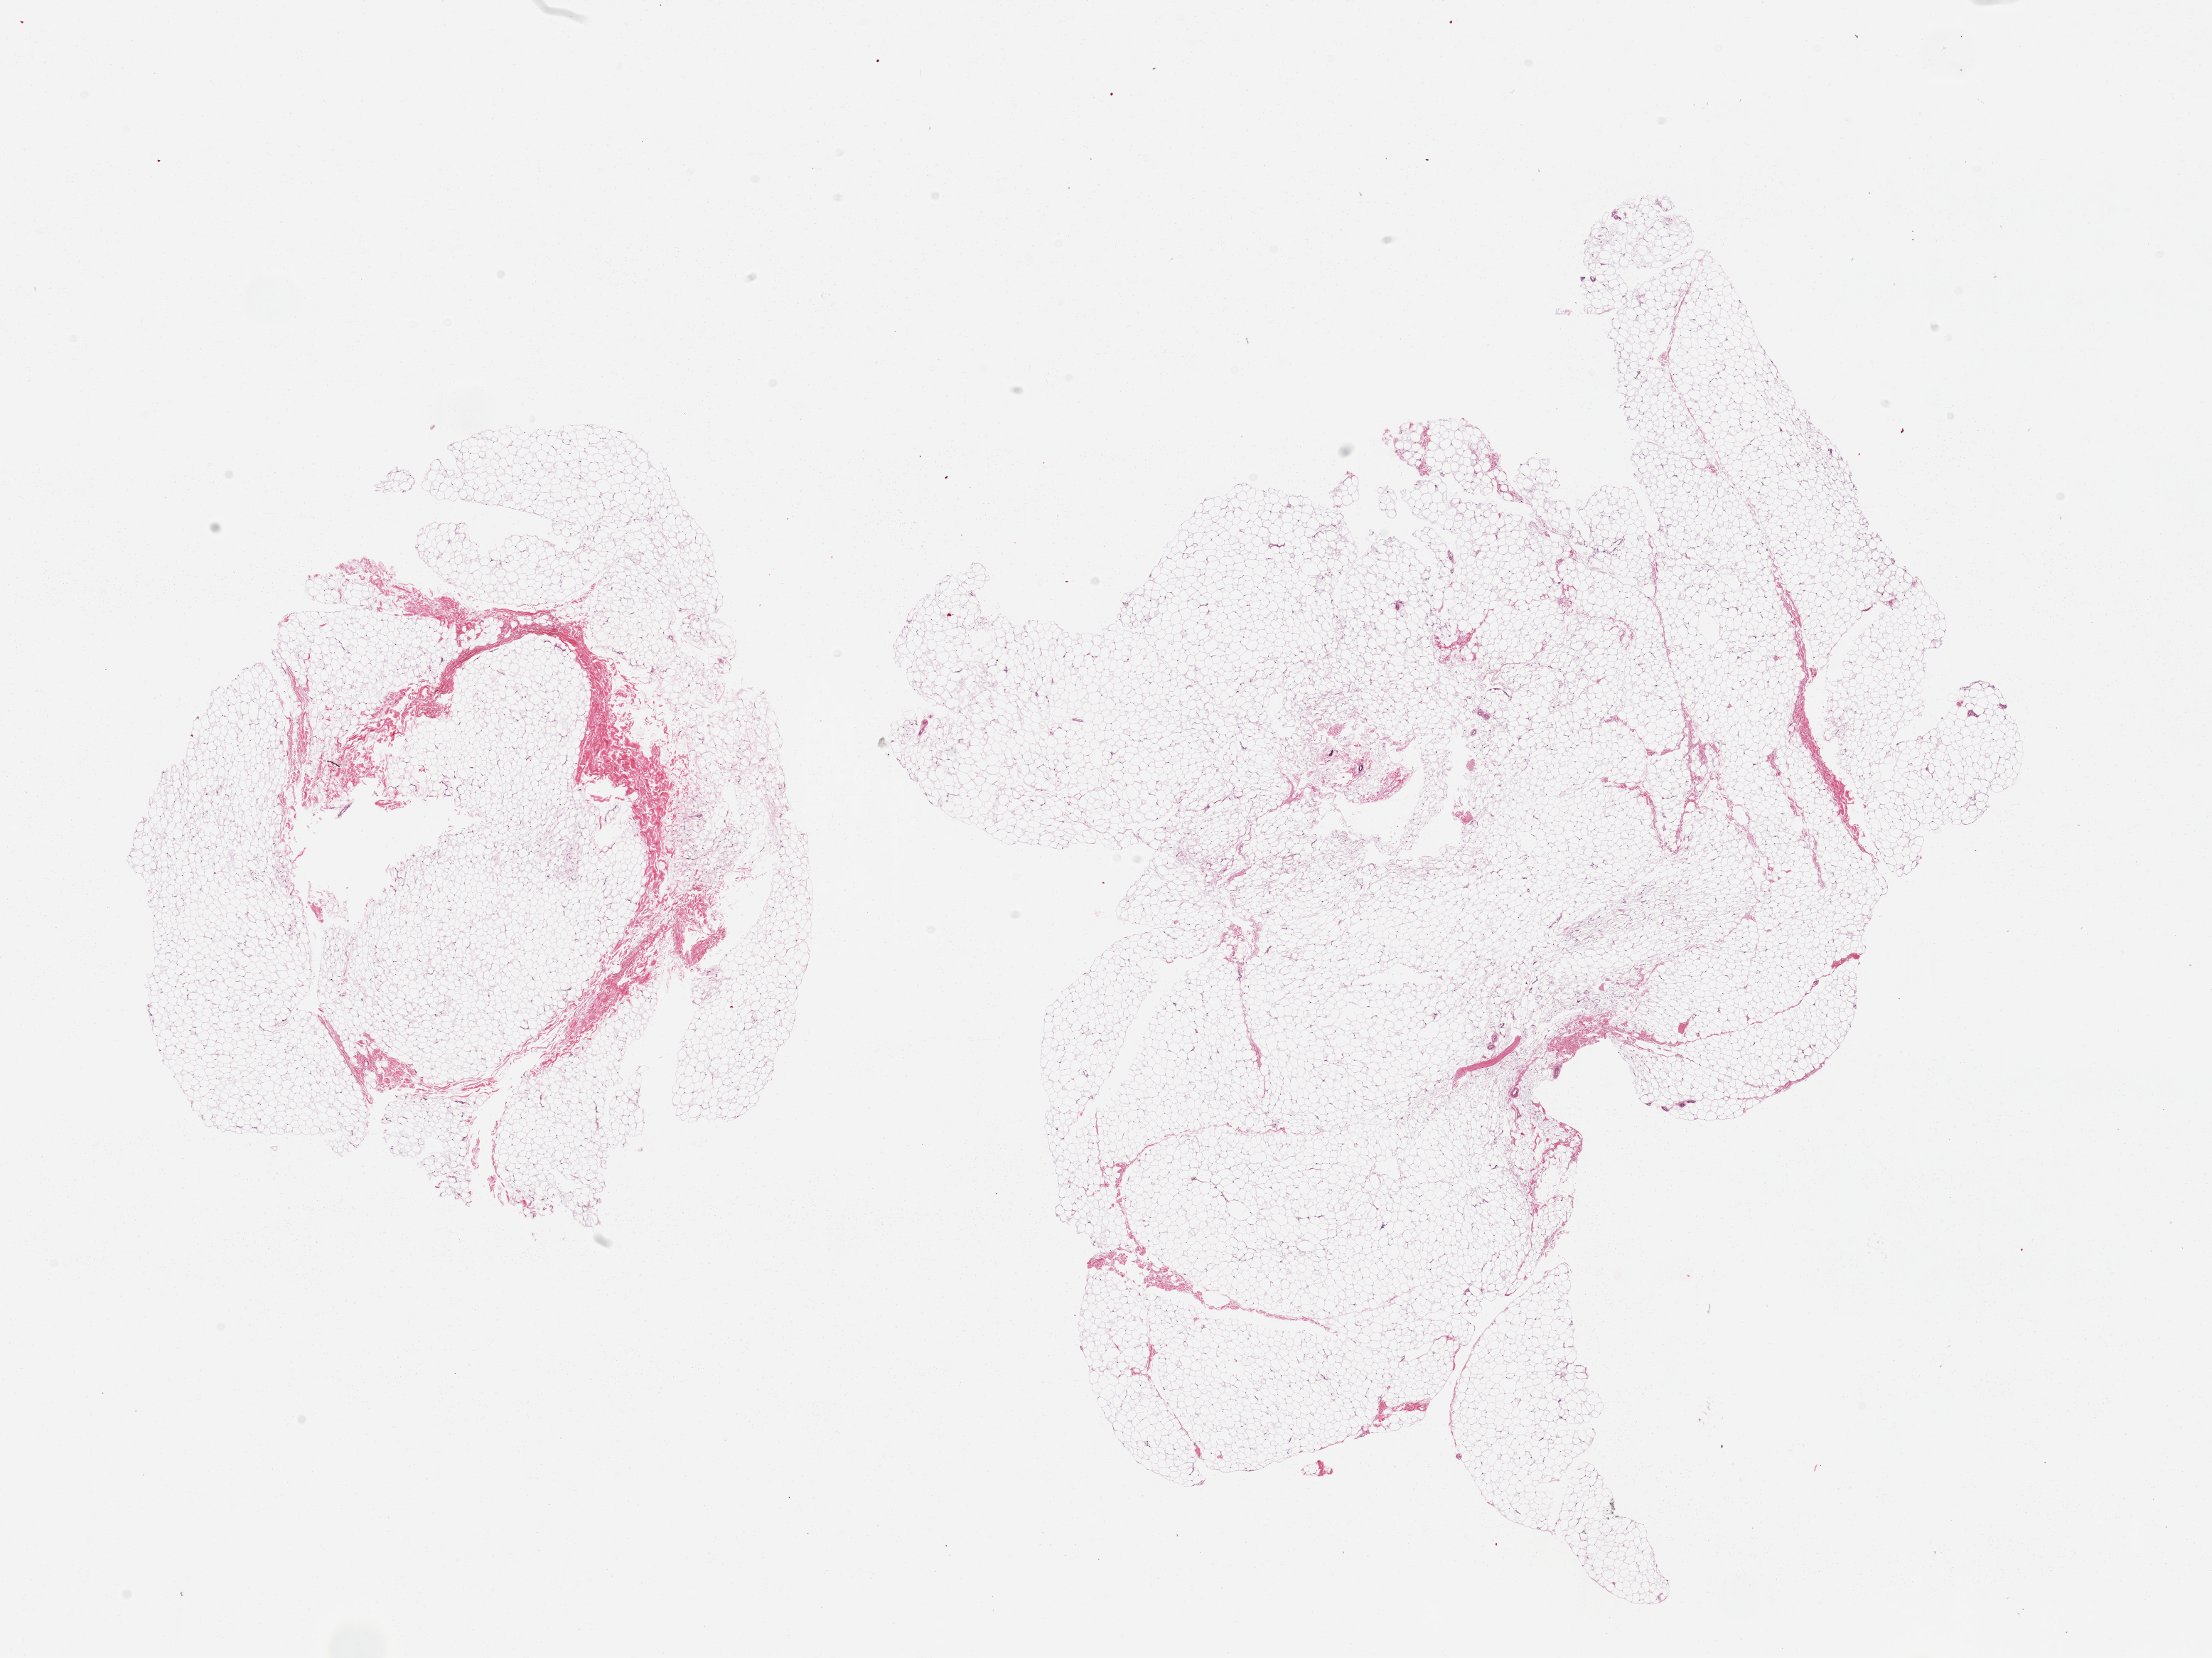
Digitized hematoxylin and eosin (H&E)-stained section, brightfield, low-resolution overview of the scanned area, about 24.6 x 18.4 mm (from a 20x scan); PAXgene-fixed, paraffin-embedded tissue; section of breast (target tissue); donor tissue sample. Donor sex: male.
* reviewer comment on this tissue sample: 2 pieces; 2 small ducts in adipose tissue with <2% fibrous content